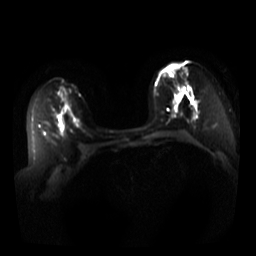
Breast MRI, one axial slice. Position 18 of 44 along the scan axis. Diffusion-weighted series; image 2 of 4 stored at this slice position (different b-values; order by instance number). 3 T. 5 mm slice thickness. 256 × 256 image matrix, field of view 340 × 340 mm. Female patient.
Structures marked on this image (expert manual segmentation):
- tumour on diffusion-weighted imaging: bounding box [x1, y1, x2, y2] px = [167, 63, 184, 97]